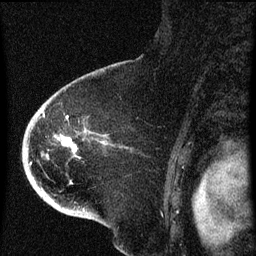
Breast MRI (dynamic contrast-enhanced), one sagittal slice; slice 47 of 60 in the series (ordered by position); dynamic contrast-enhanced series, image 2 of 4 at this slice position (ordered by acquisition); 1.5 T; TE 4.2 ms, TR 8 ms; 2 mm slice thickness; 256 × 256 image matrix, field of view 180 × 180 mm. Patient: female, 71 years.
Annotated regions visible in this slice (semi-automatically segmented with operator editing):
- analysis volume of interest (the breast-tissue region the enhancement analysis was run in; not a lesion): bounding box (x1, y1, x2, y2) in pixels: (32, 86, 111, 205)
- tumour enhancement mask (voxels above the 70 % enhancement threshold inside the analysis volume of interest): (43, 114, 105, 159)